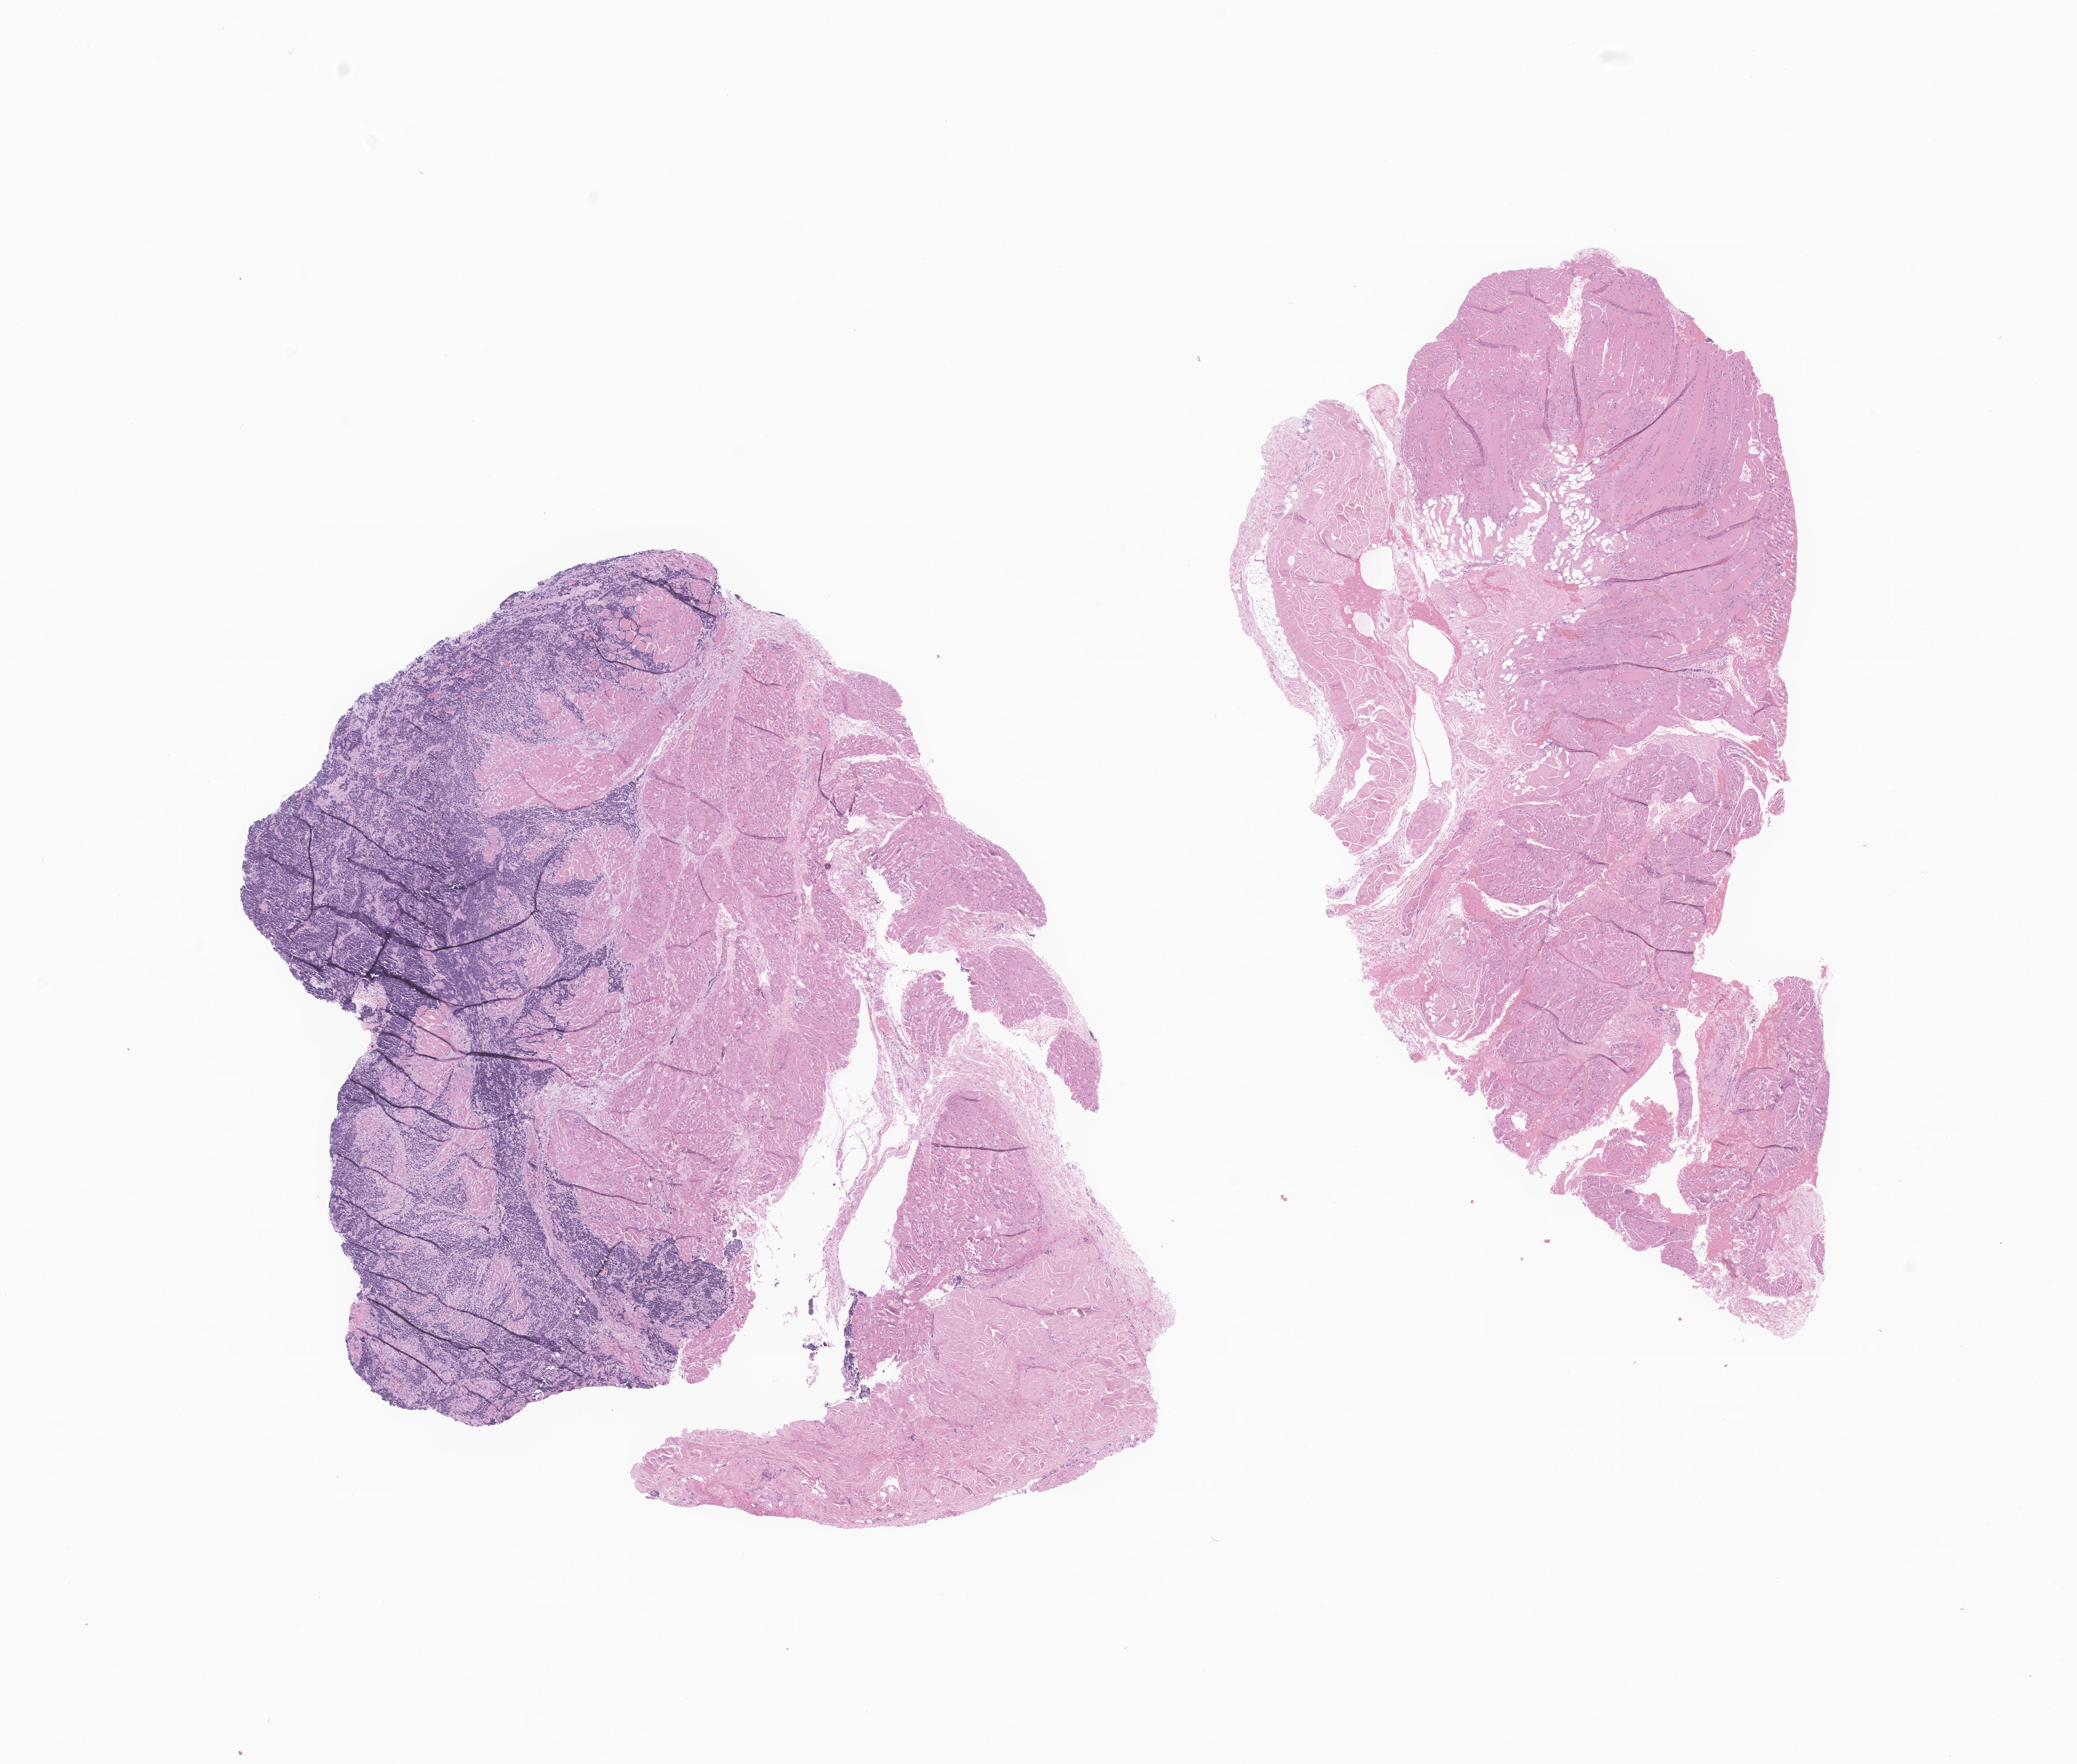
Digitized haematoxylin and eosin-stained section of tumor tissue from the mediastinum, a low-resolution overview of the entire scanned area, about 16.0 x 13.6 mm, formalin-fixed paraffin-embedded section. Patient male; age 138 months.
• diagnosis: Alveolar rhabdomyosarcoma